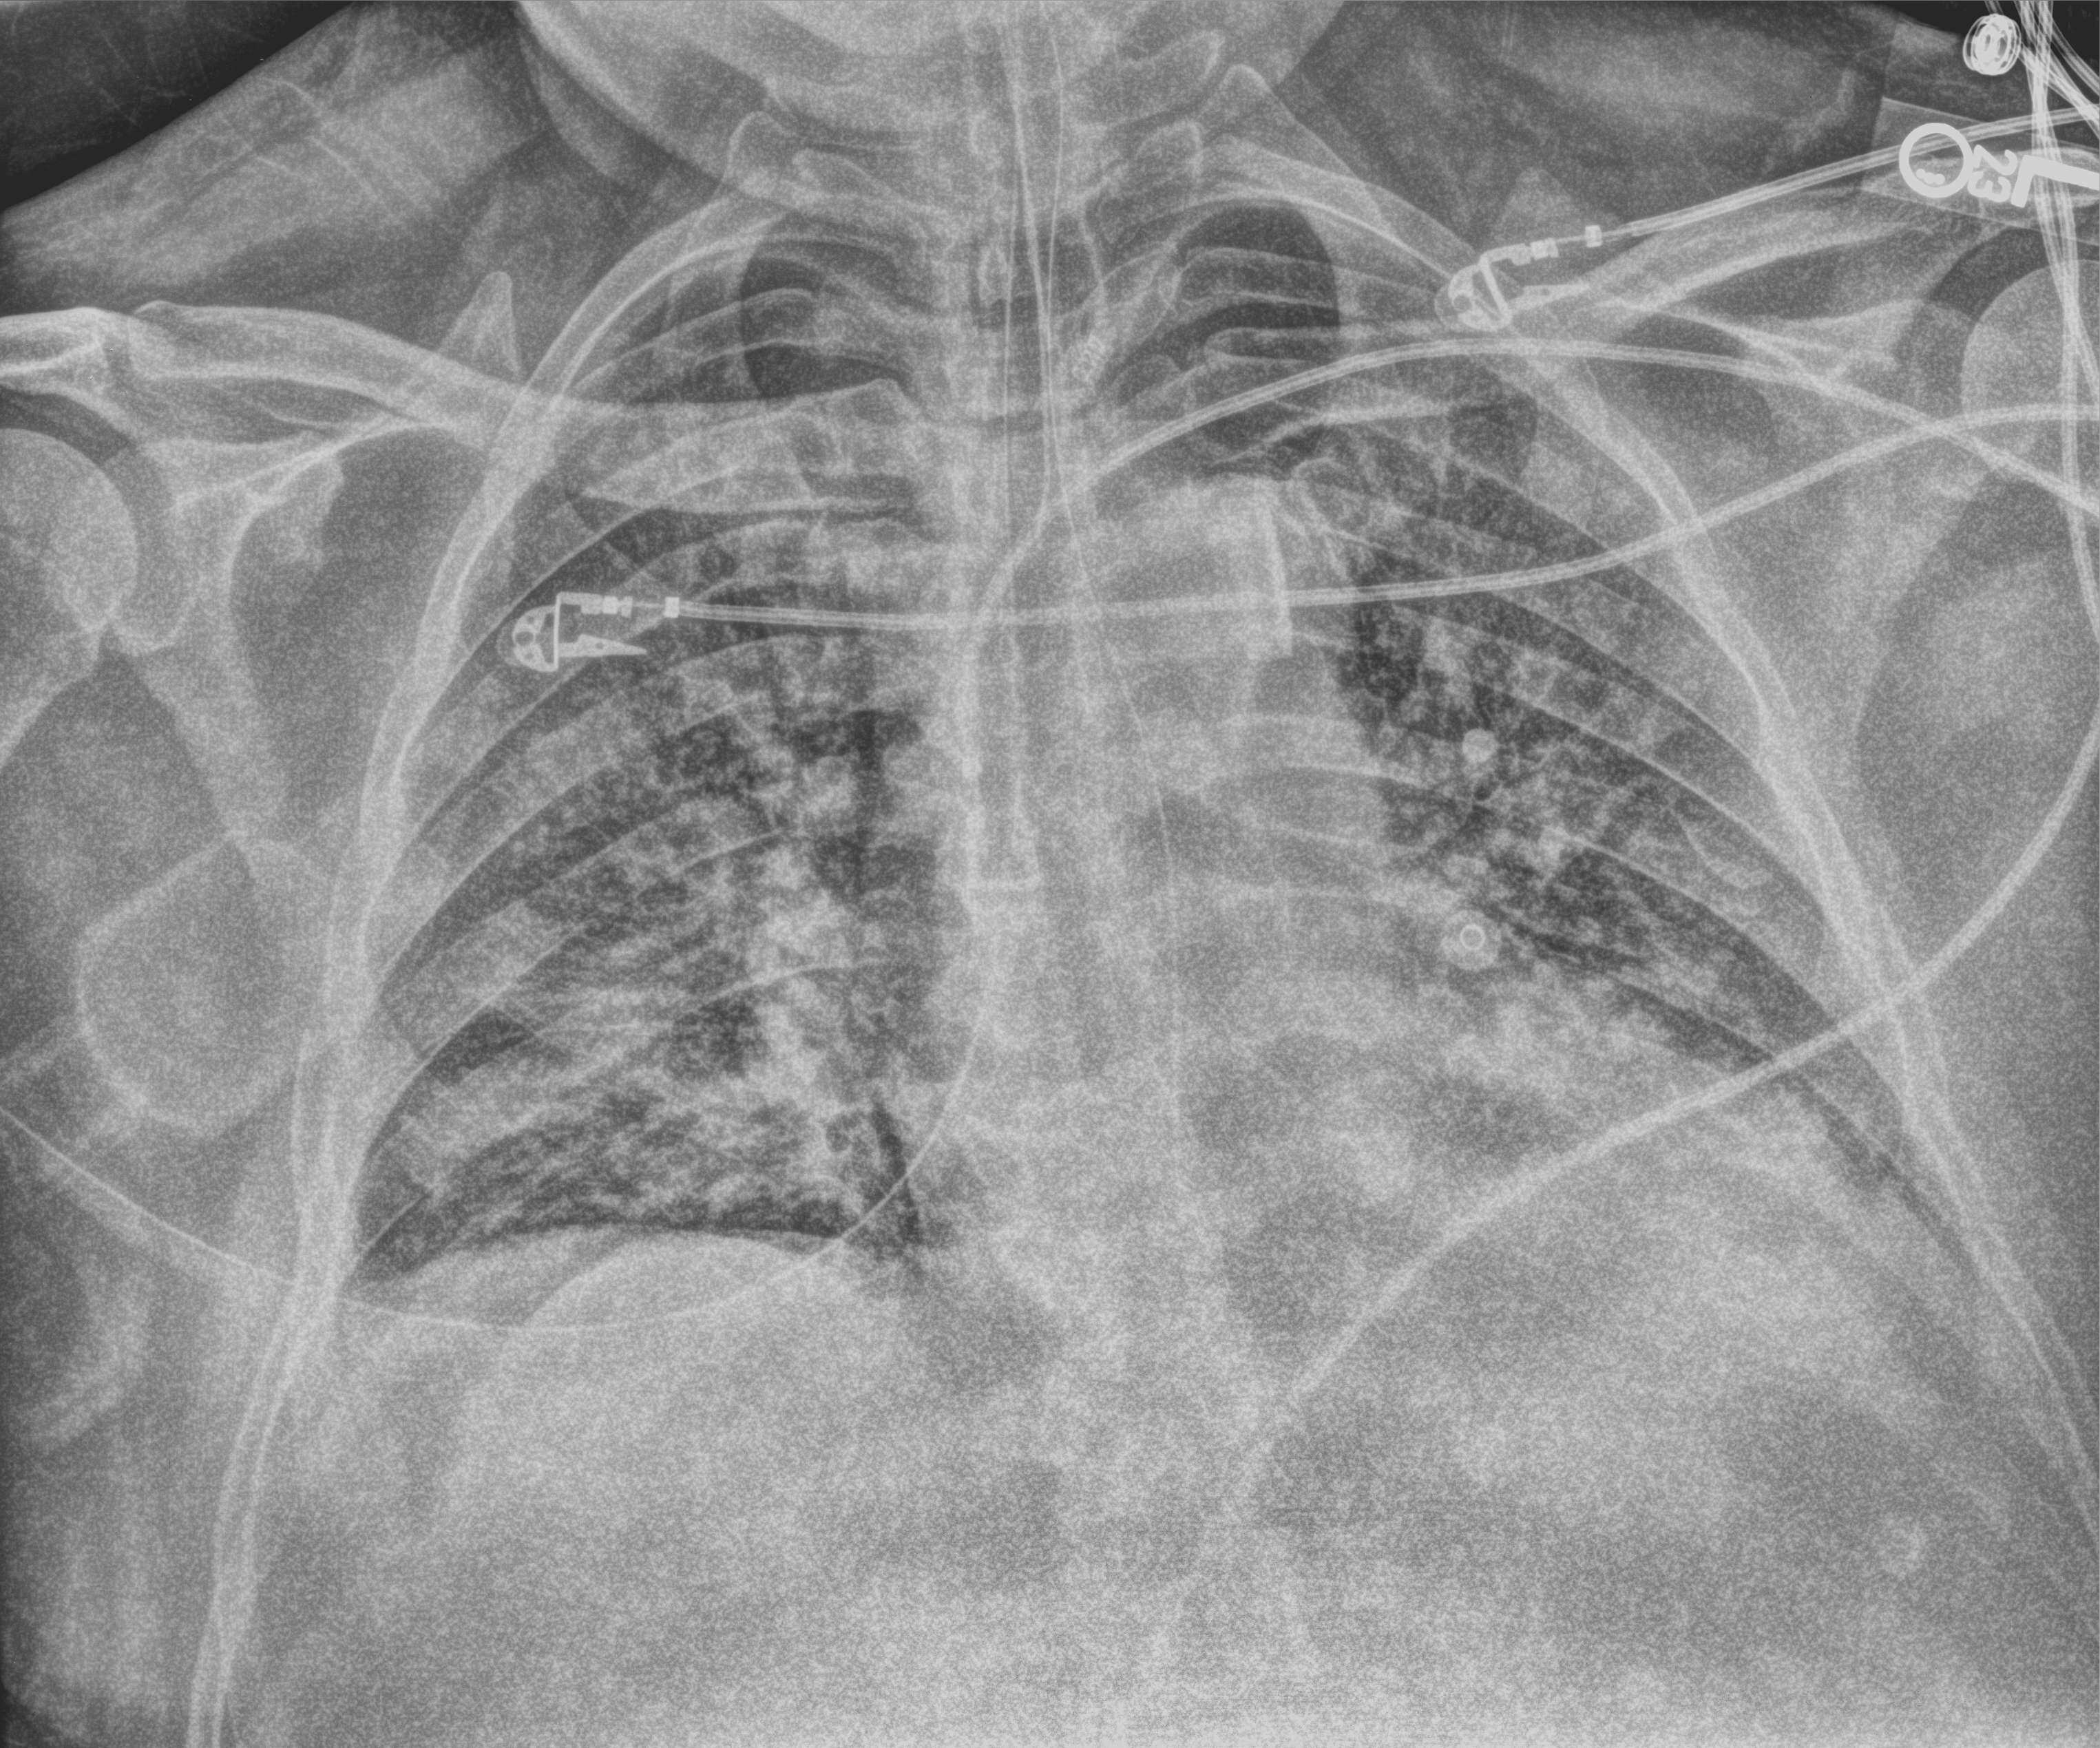
Chest X-ray (portable), anteroposterior (AP) projection. Patient hospitalised with COVID-19; male, aged 60–74 years.
From the hospital-stay record, not from the radiograph (when in the stay this image was taken is not recorded): COPD (admission record): no; mechanically ventilated during this hospital stay: yes.